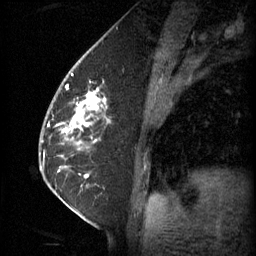
Breast MRI (dynamic contrast-enhanced), one sagittal slice. Position 27 of 60 along the scan axis. 3 images stored at this slice position (order not interpretable as contrast timing). 1.5 T. TE 4.2 ms, TR 11 ms. 2 mm slice thickness. 256 × 256 image matrix, field of view 180 × 180 mm. Patient: female, 62 years.
Outlined on this slice (semi-automatically segmented with operator editing):
- analysis volume of interest (the breast-tissue region the enhancement analysis was run in; not a lesion): bounding box [x1, y1, x2, y2] px = [55, 72, 113, 133]
- tumour enhancement mask (voxels above the 70 % enhancement threshold inside the analysis volume of interest): [63, 90, 100, 133]